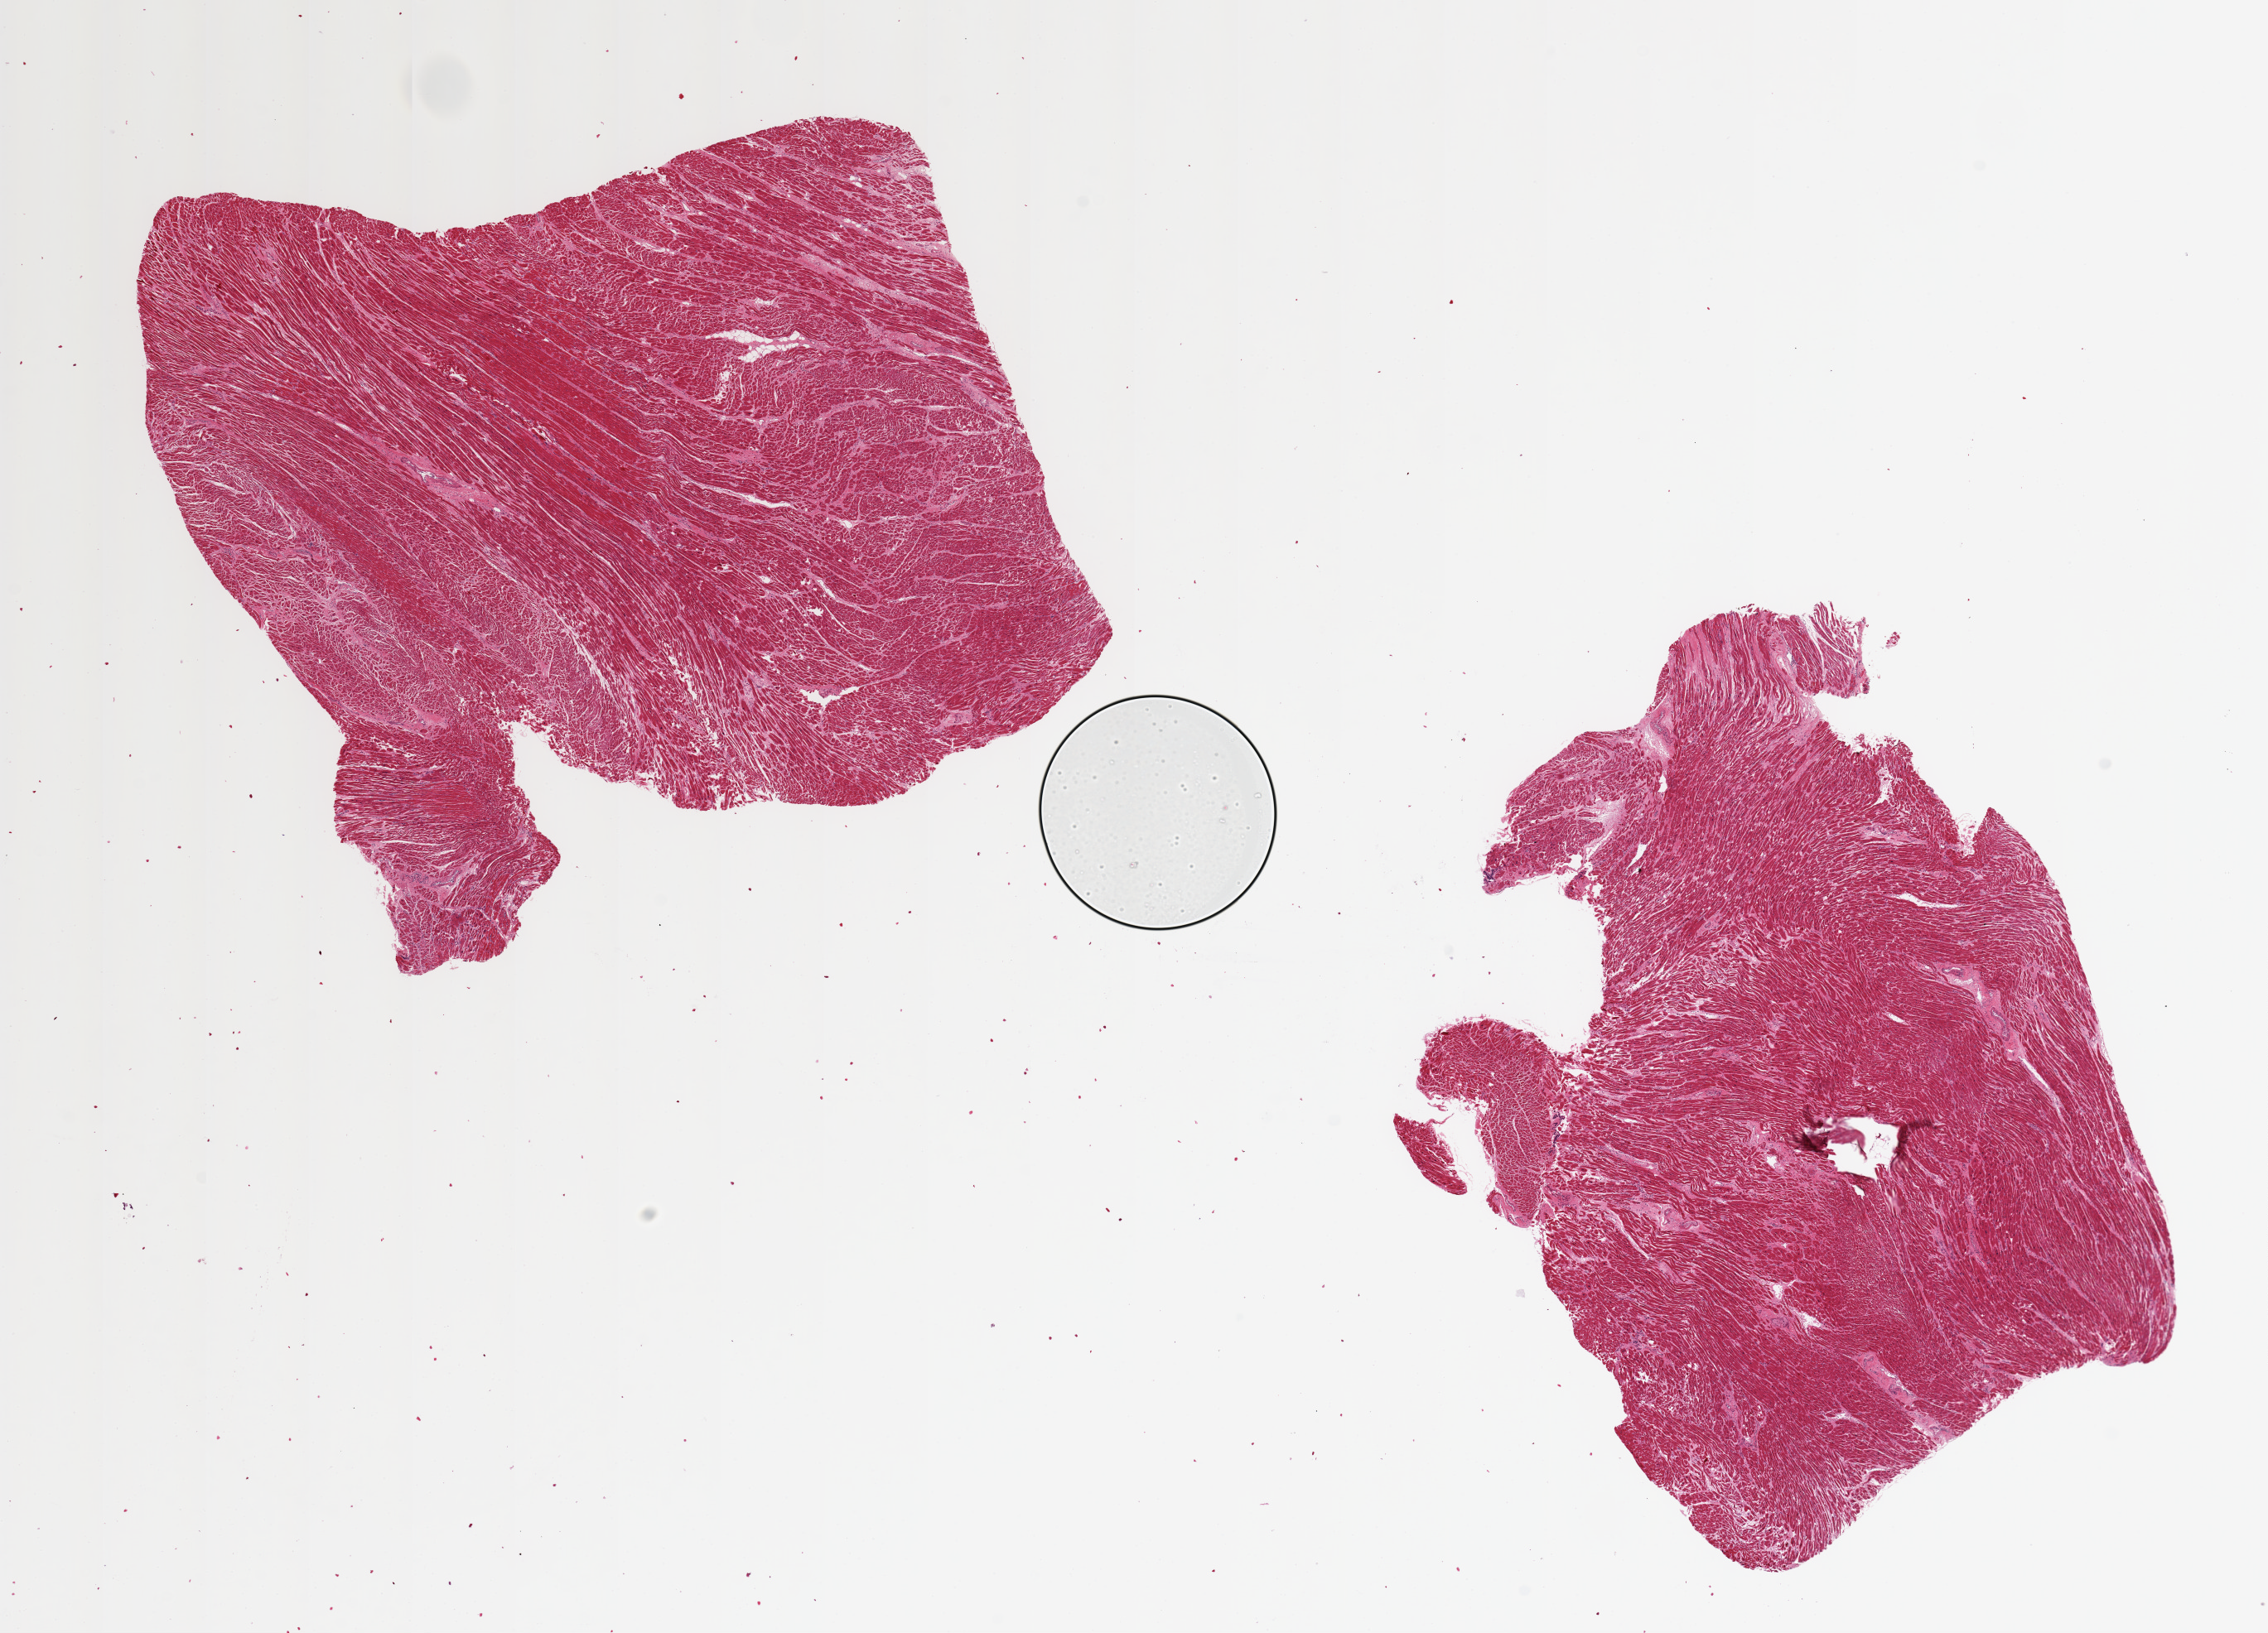
Hematoxylin and eosin (H&E) whole-slide image — whole scanned area (about 21.7 x 15.6 mm, slide scanned at 20x) shown as a low-resolution overview. PAXgene-fixed, paraffin-embedded tissue. Section of heart (target tissue). Donor tissue sample. Donor sex: female.
Pathologist's review note for this sample: 2 pieces, 8x8 & 8x6mm; hypereosinophilia consistent with early myocardial infarct.